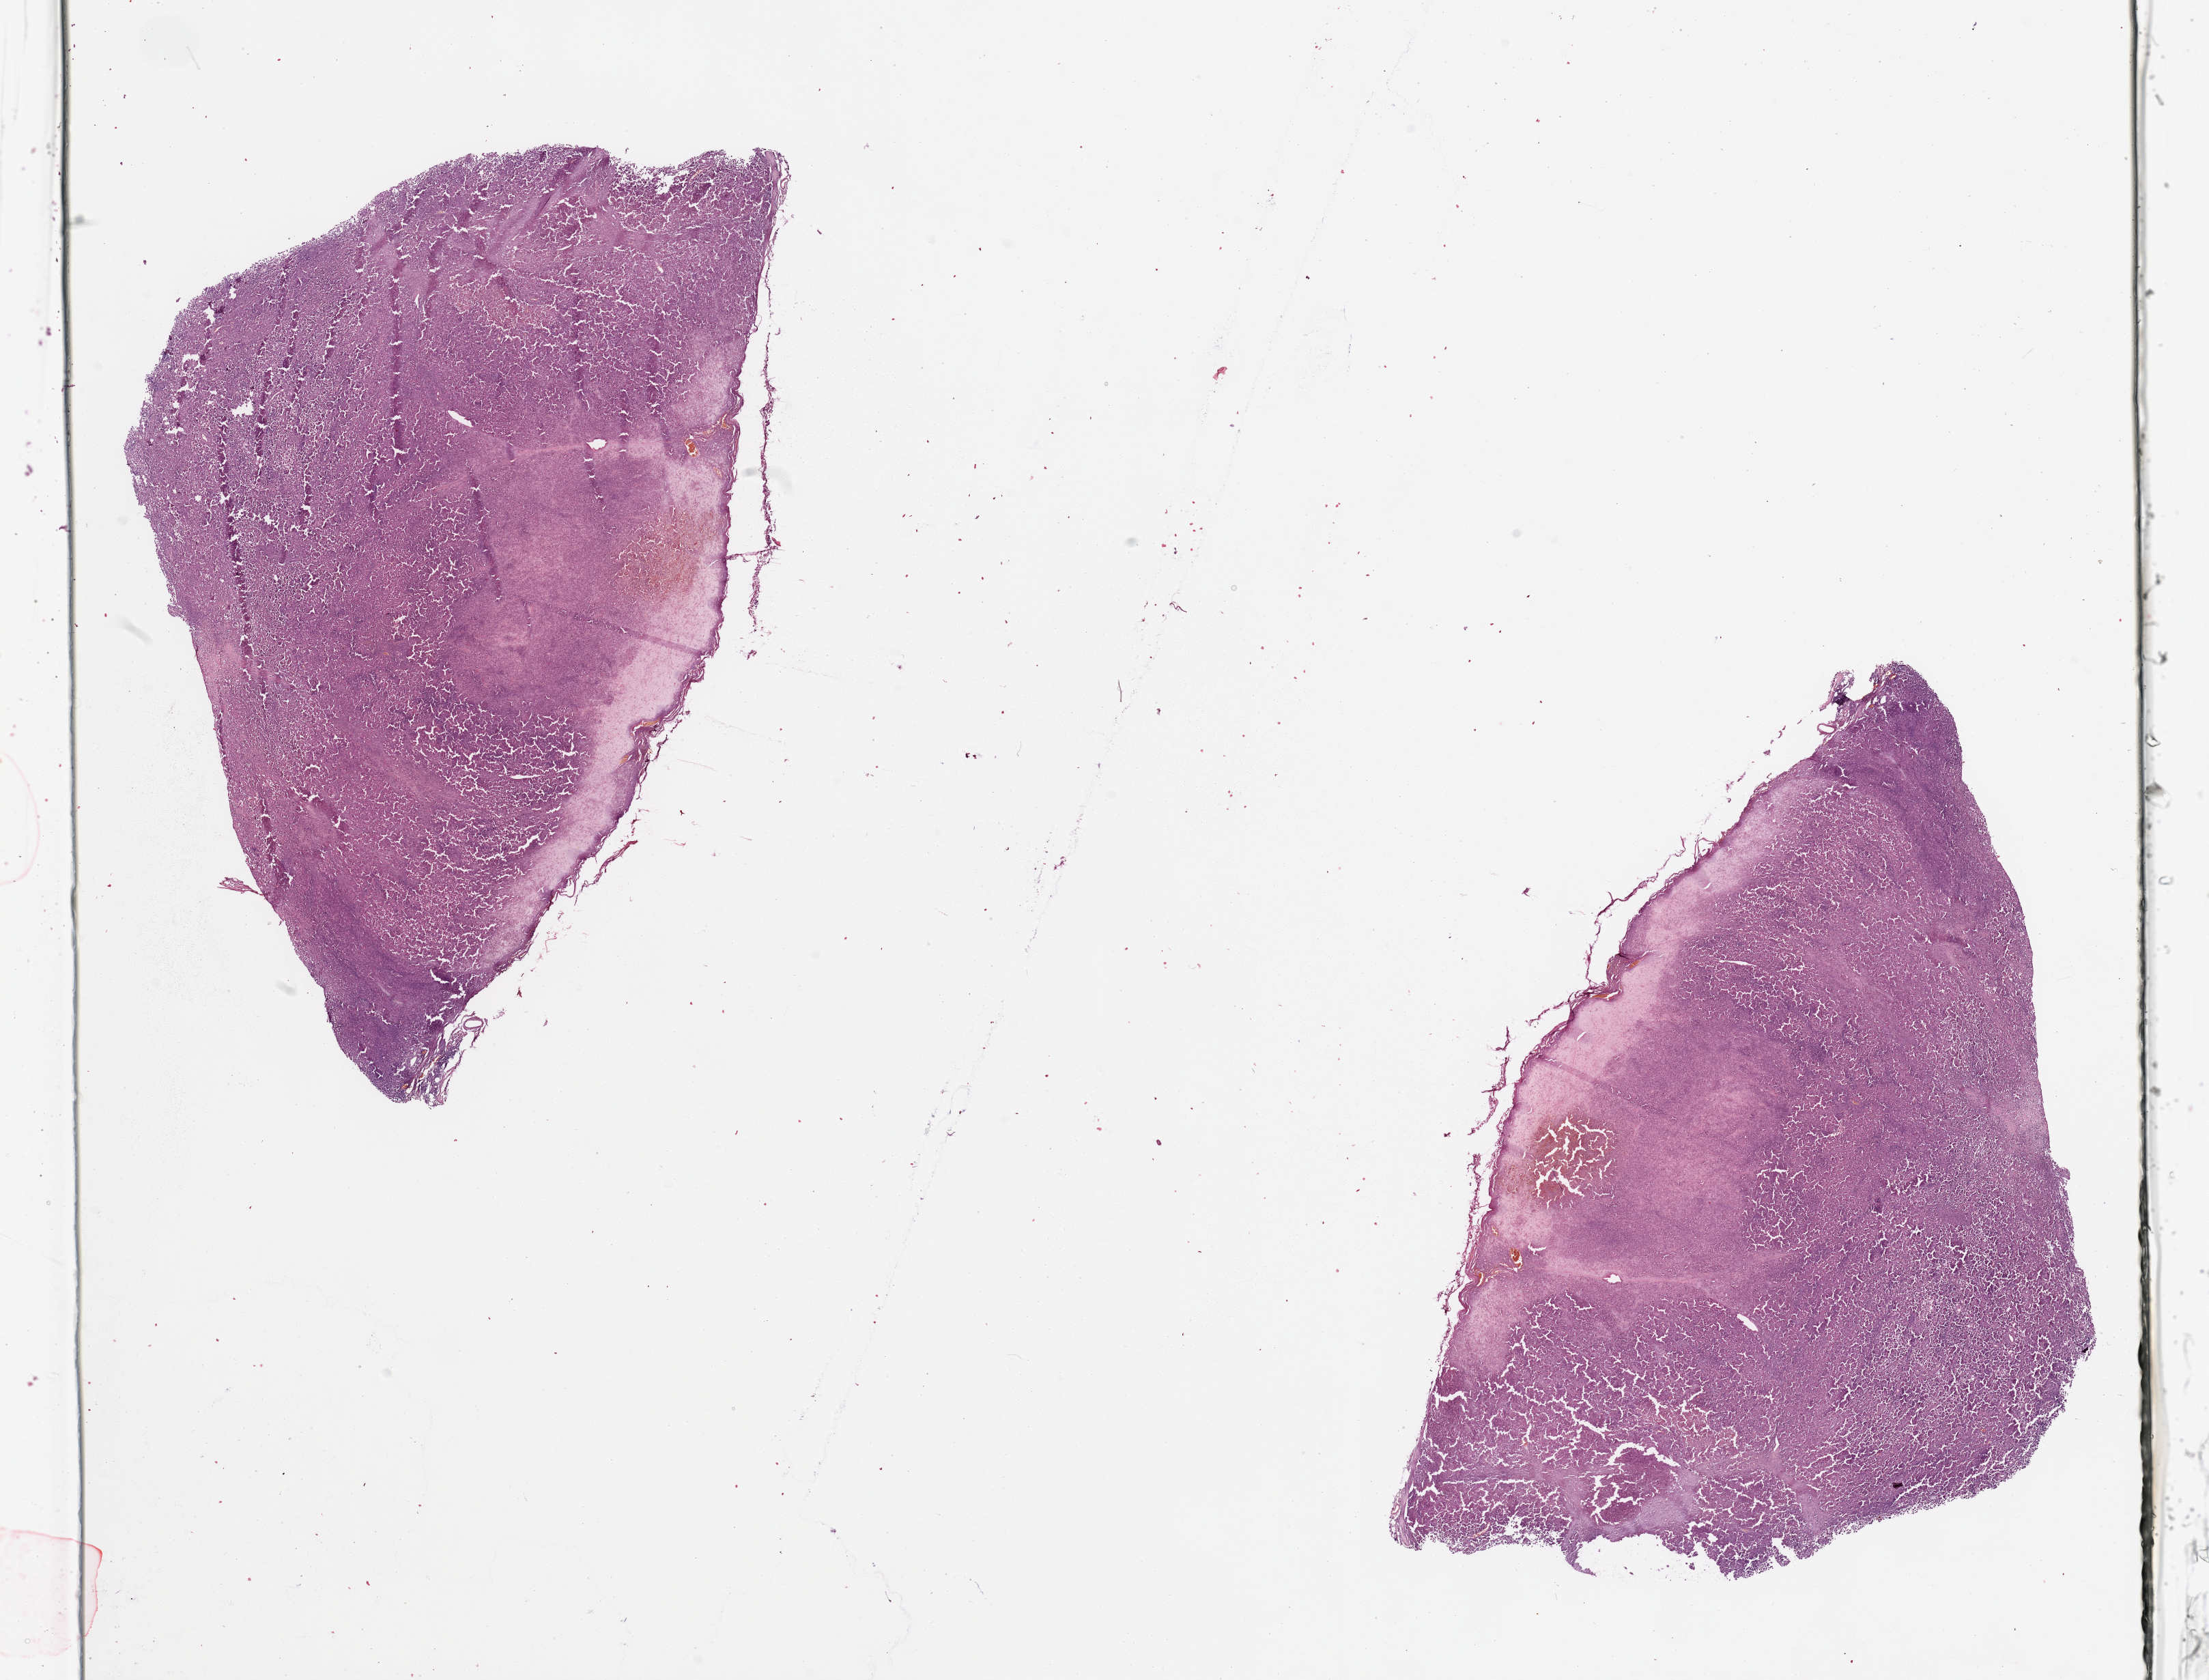
Digitized H&E tissue section (whole slide) — whole scanned area (about 25.6 x 19.5 mm) shown as a low-resolution overview. Melanoma tumour tissue; sampled site not recorded. 32-year-old male patient.
* primary tumour site (as recorded): extremities
* histologic diagnosis: Malignant melanoma, NOS
* AJCC pathologic stage: IIB